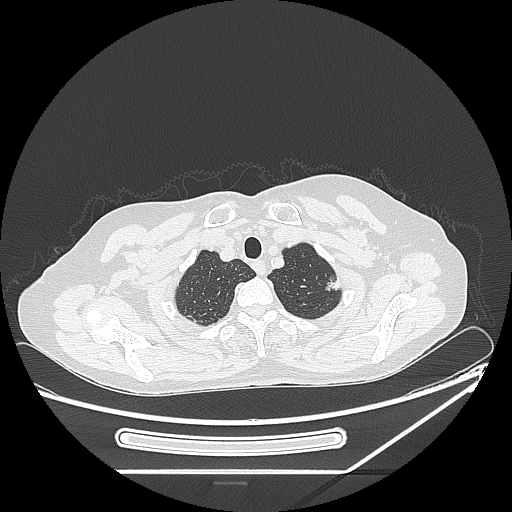
Chest CT, one axial slice. Slice 215 of 250 in the series (ordered by position). 120 kVp. Lung window (W 1500 / L -600 HU). 1.25 mm slice thickness. 512 × 512 image matrix, field of view 409 × 409 mm. Patient: female, 57 years. From the clinical record (not read from this slice): clinical TNM (as recorded): T1c N0 M0; histopathological grade: G2-3.
Annotated regions visible in this slice (bounding box drawn by a radiologist):
- lung tumour (recorded histology: adenocarcinoma): box from (x=322, y=273) to (x=342, y=296) px